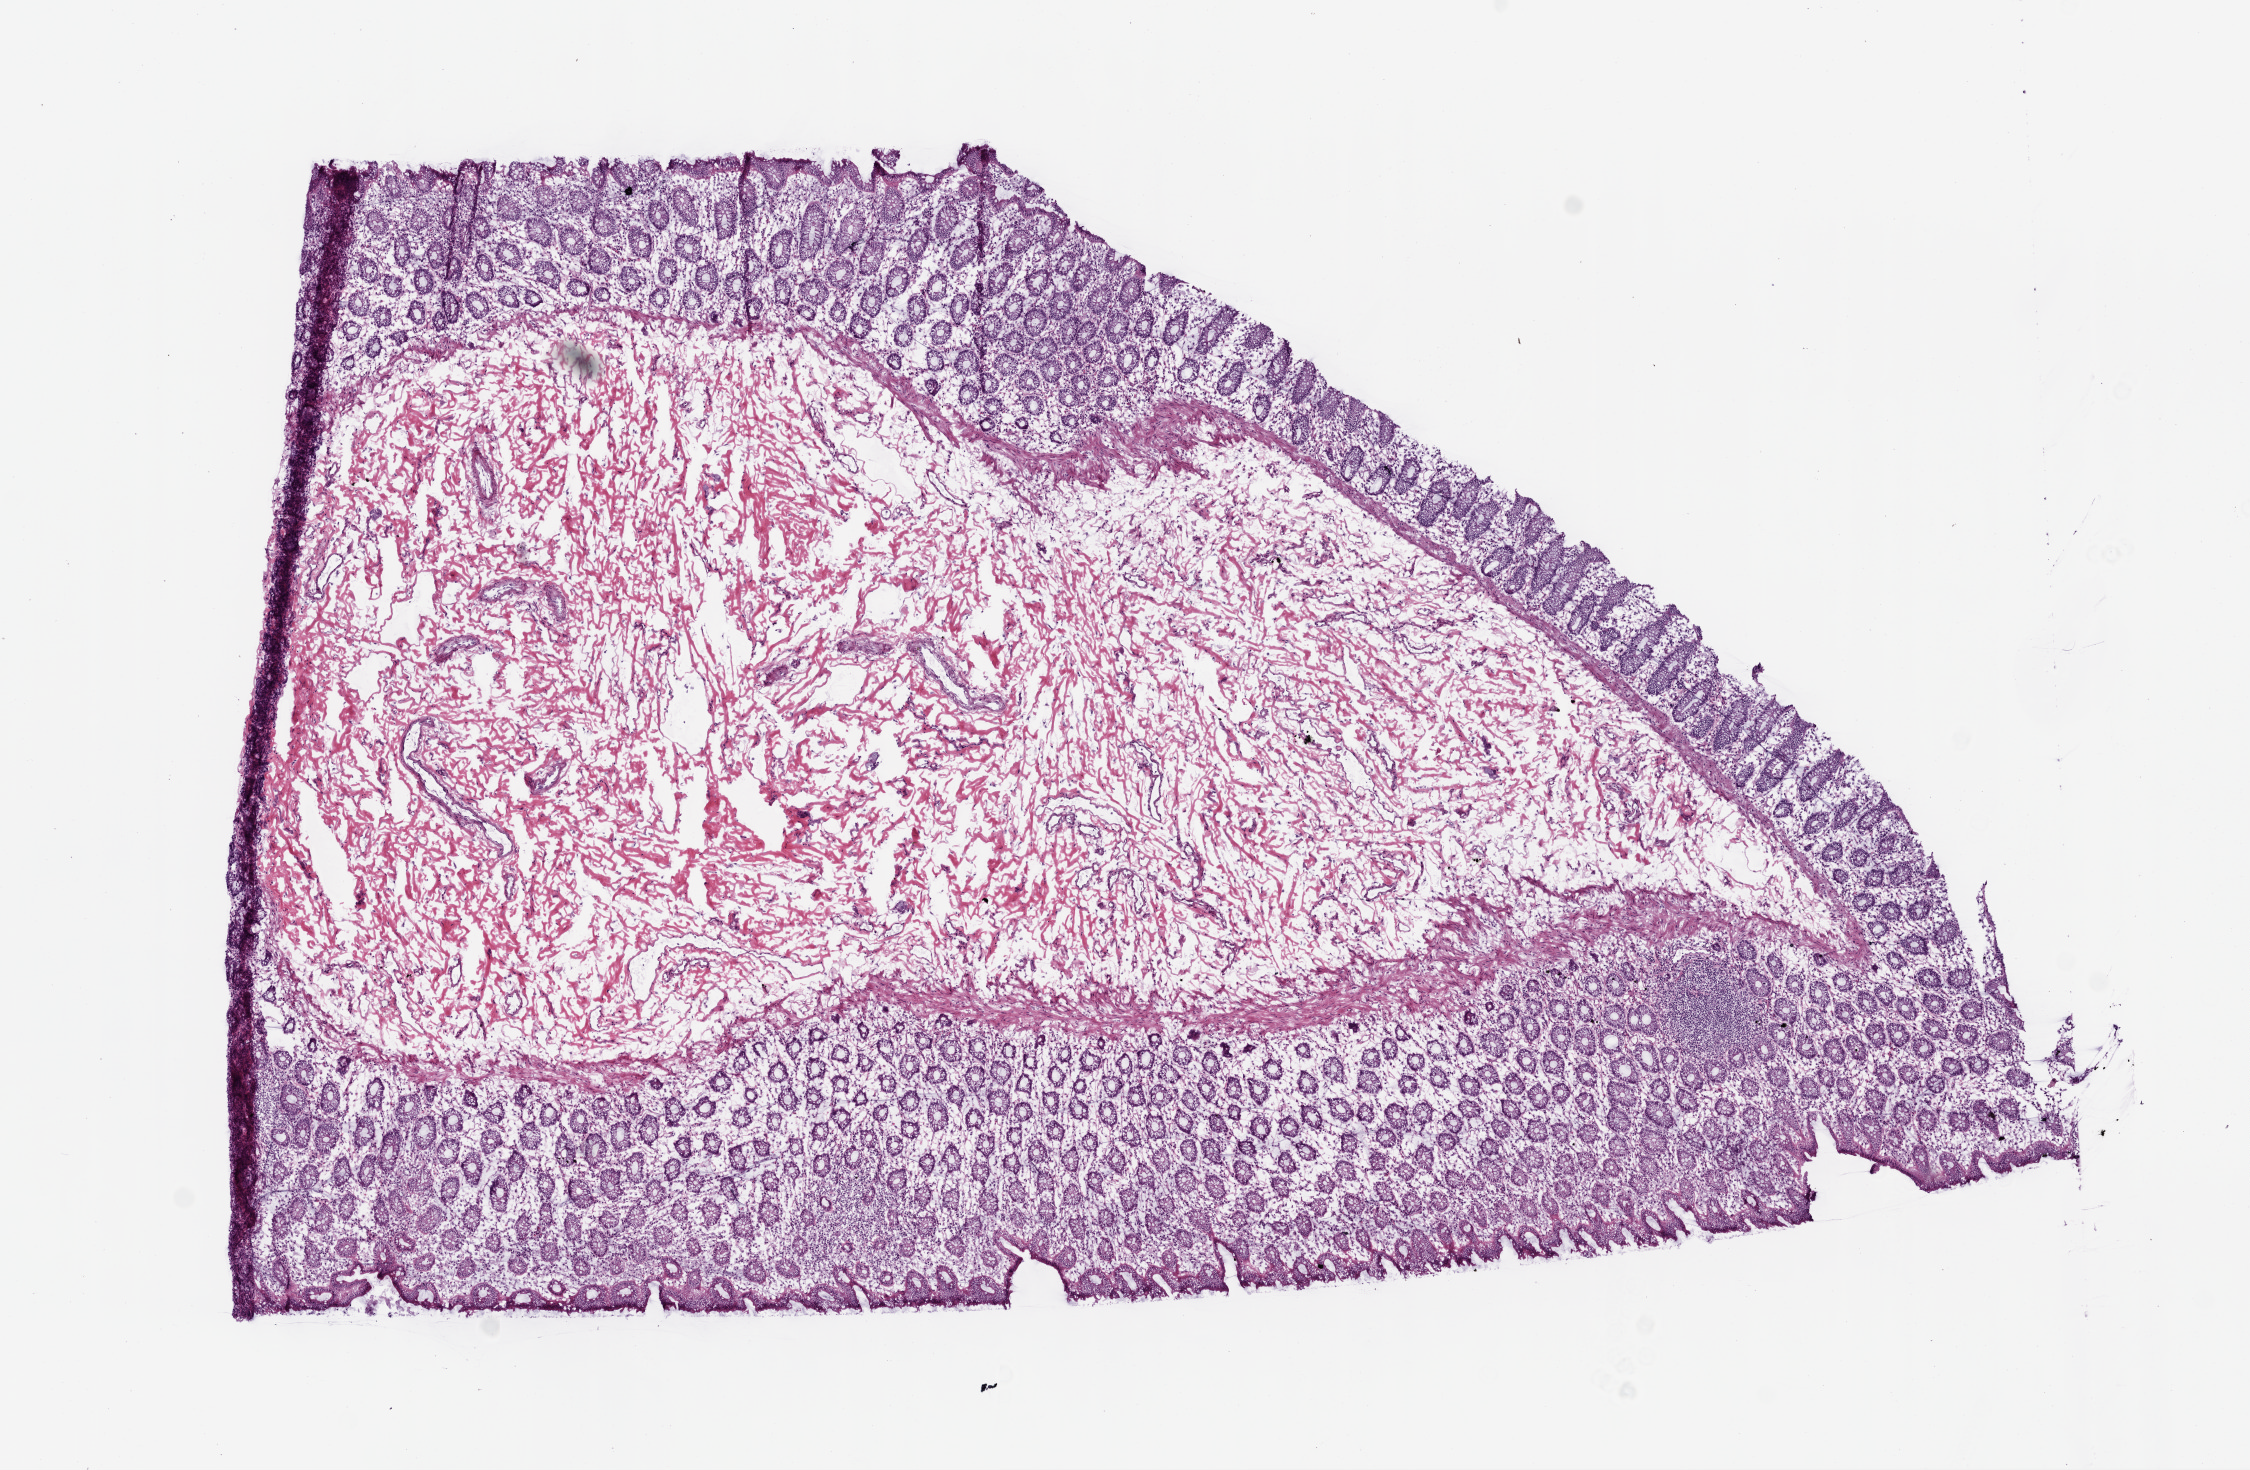
Digitized H&E tissue section (whole slide), low-resolution overview of the scanned area, about 9.0 x 5.9 mm, frozen section from the top of the tissue portion, solid tissue normal (non-tumour tissue) sample from the colon. Female, age 86 years at initial diagnosis.
• this section: solid tissue normal sample (biorepository sample class)
• patient diagnosis: Adenocarcinoma, NOS (ascending colon)